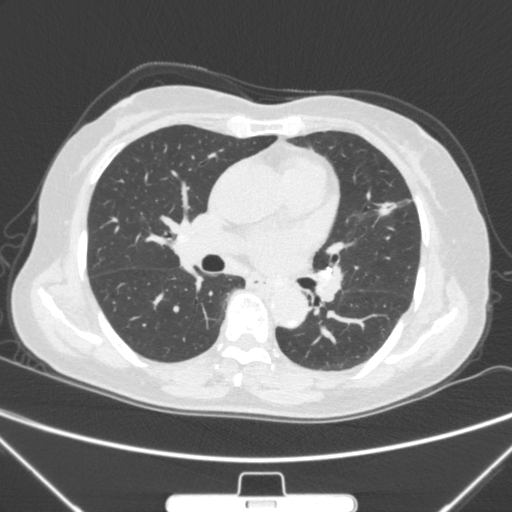
Chest CT, one axial slice; slice 151 of 300 in the series (ordered by position); 120 kVp; lung window (W 1500 / L -600 HU); 1 mm slice thickness; 512 × 512 image matrix. Female patient, age 70 years. Case-level facts recorded for this patient, not image findings: clinical TNM (as recorded): T1b N0 M0; histopathological grade: G2.
Annotated regions visible in this slice (bounding box drawn by a radiologist):
- lung tumour (recorded histology: adenocarcinoma): box from (x=366, y=192) to (x=398, y=230) px